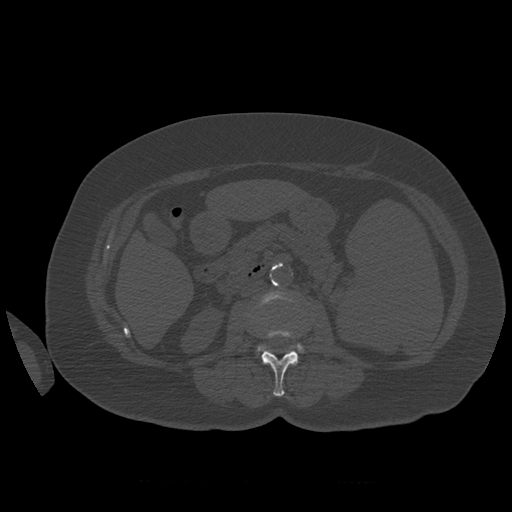
CT including the spine, one axial slice. Position 245 of 399 along the scan axis. 120 kVp. Bone window (W 1800 / L 400 HU). 1.25 mm slice thickness. 512 × 512 image matrix, field of view 404 × 404 mm. Patient age 81 years. From the clinical record (not read from this slice): primary cancer: renal.
Outlined on this slice (semi-automatically segmented with operator editing):
- L2 vertebra: box from (x=261, y=330) to (x=299, y=397) px
- L3 vertebra: (x=258, y=292)–(x=304, y=353)